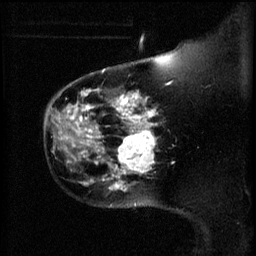
Breast MRI (dynamic contrast-enhanced), one sagittal slice. Slice 47 of 60 in the series (ordered by position). 3 images stored at this slice position (order not interpretable as contrast timing). 1.5 T. TE 4.2 ms, TR 11 ms. 256 × 256 image matrix. Patient: female, 44 years.
Annotated regions visible in this slice (semi-automatic segmentation, software-assisted and operator-edited):
- analysis volume of interest (the breast-tissue region the enhancement analysis was run in; not a lesion): bounding box [x1, y1, x2, y2] px = [110, 124, 159, 179]
- tumour enhancement mask (voxels above the 70 % enhancement threshold inside the analysis volume of interest): [116, 124, 157, 179]